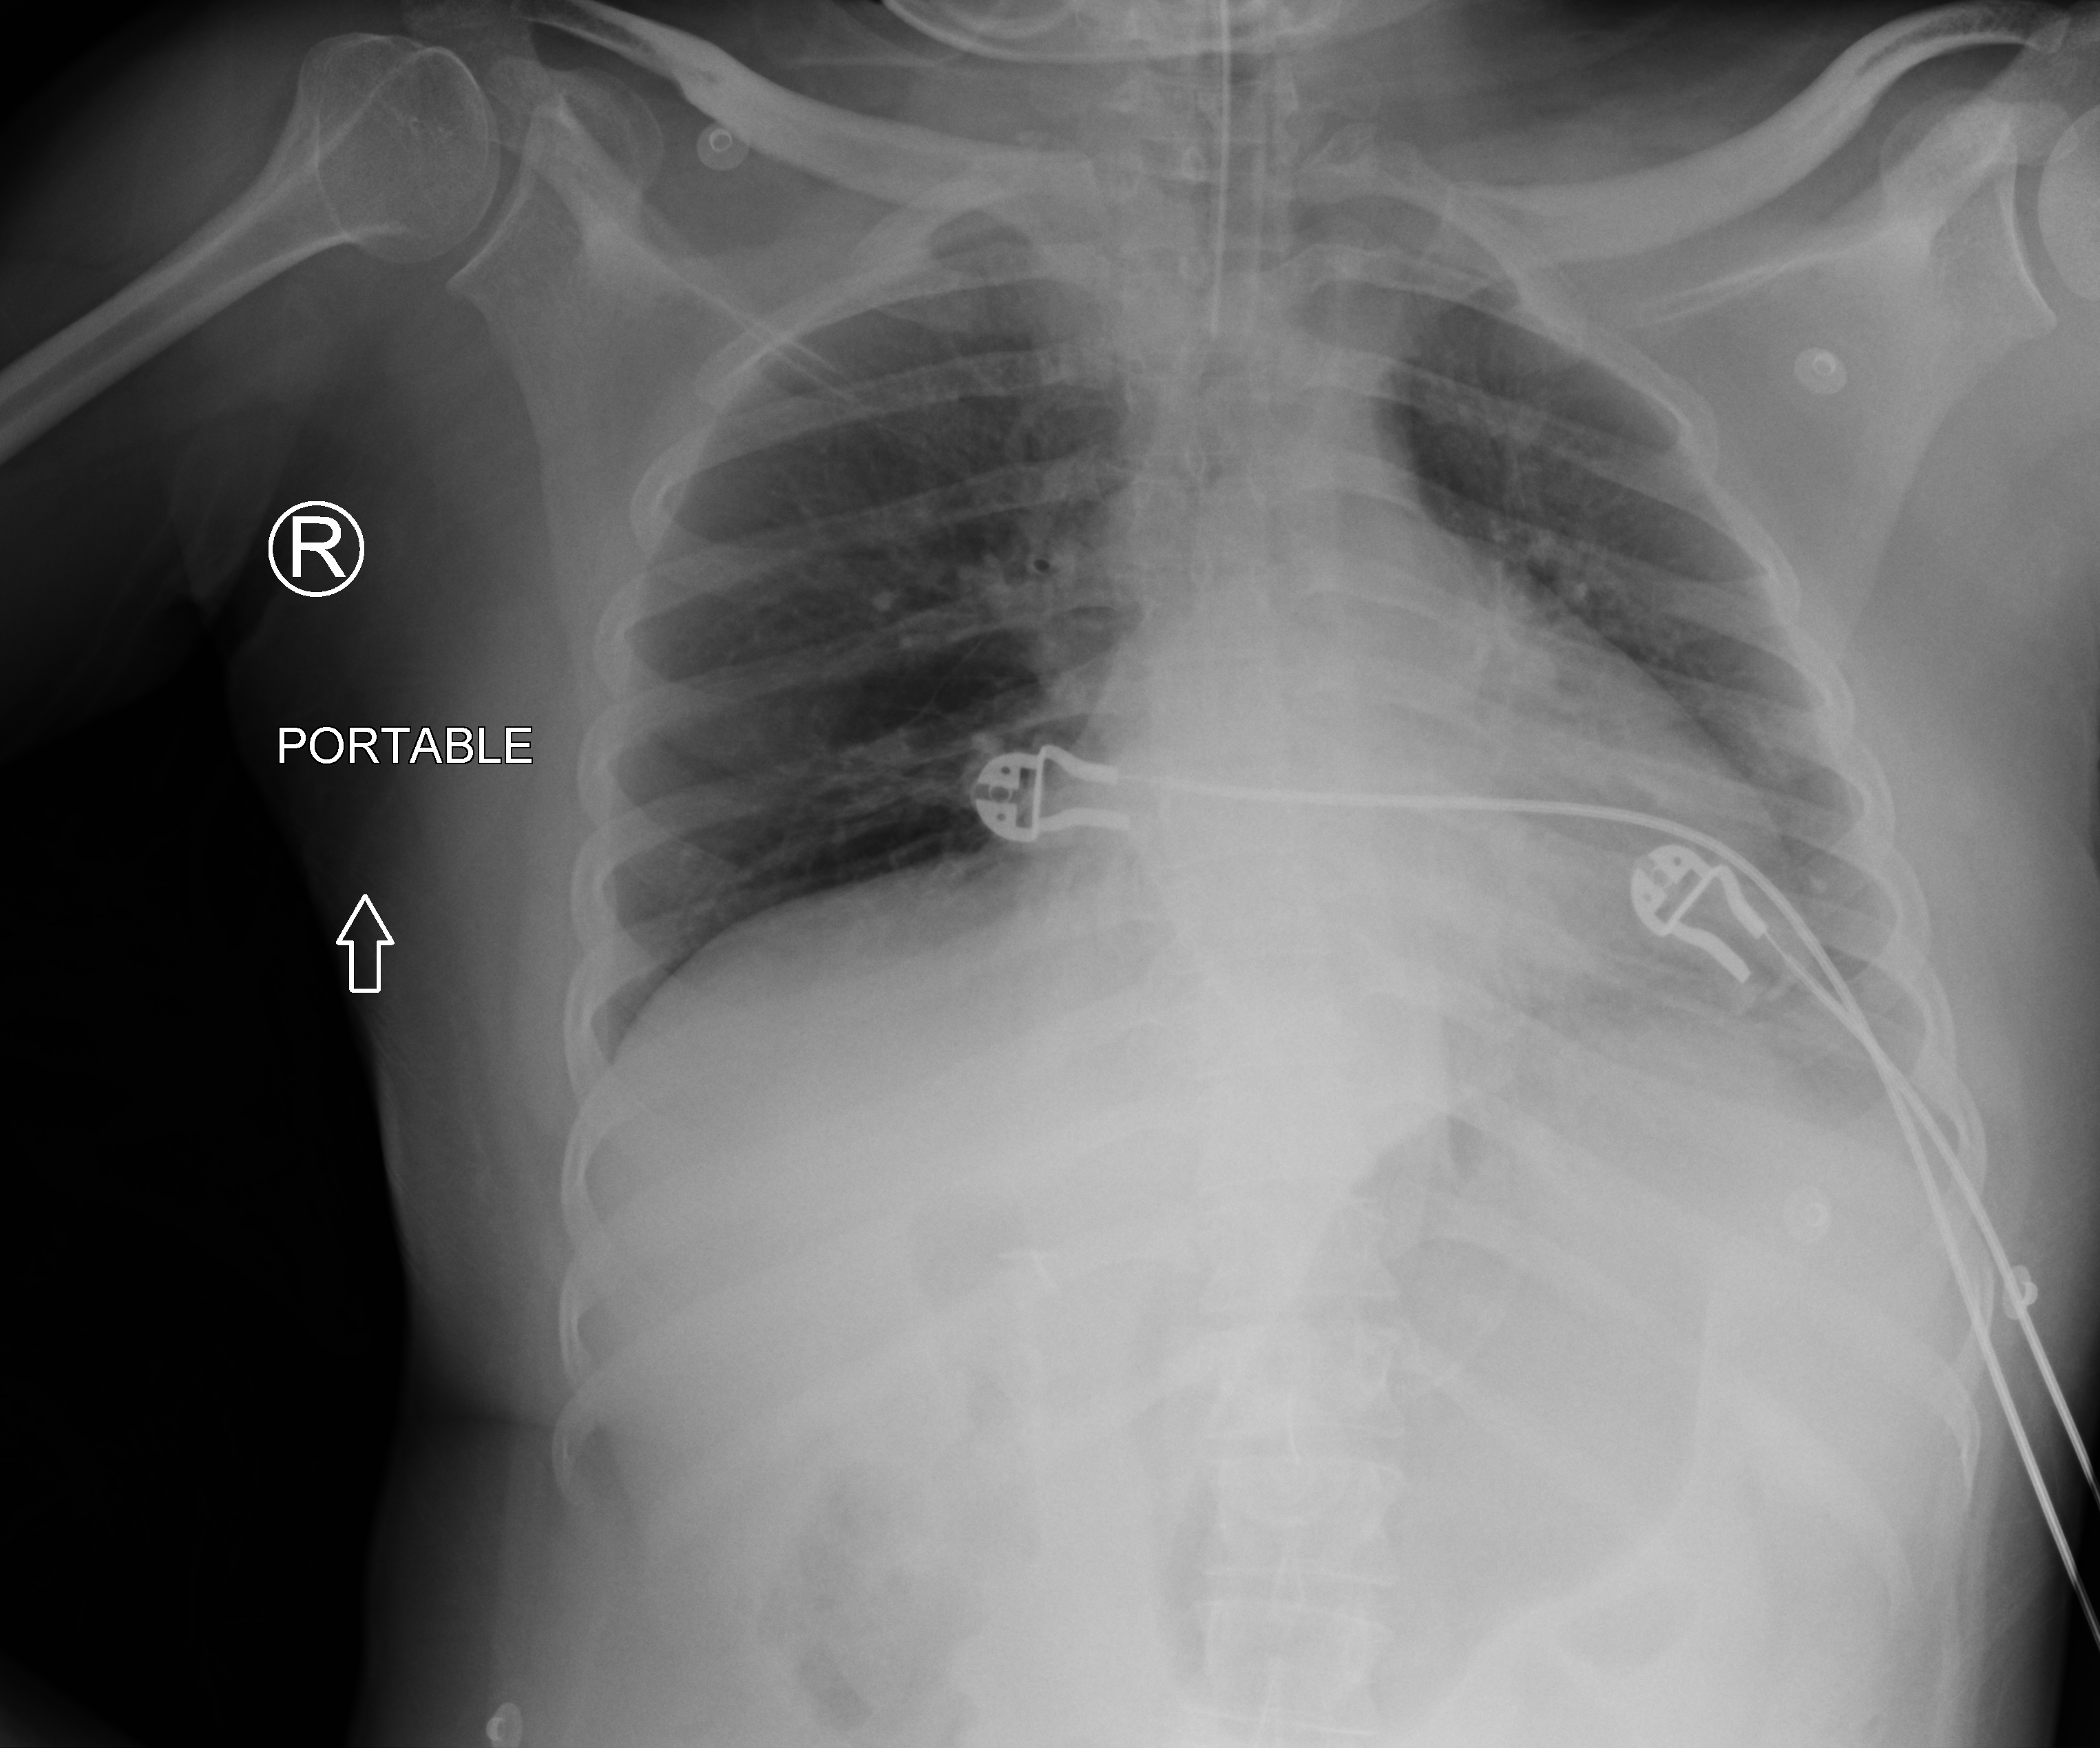
Chest X-ray (portable); anteroposterior (AP) projection. Patient hospitalised with COVID-19; male, aged 18–59 years.
From the hospital-stay record, not from the radiograph (when in the stay this image was taken is not recorded): mechanically ventilated during this hospital stay: no.